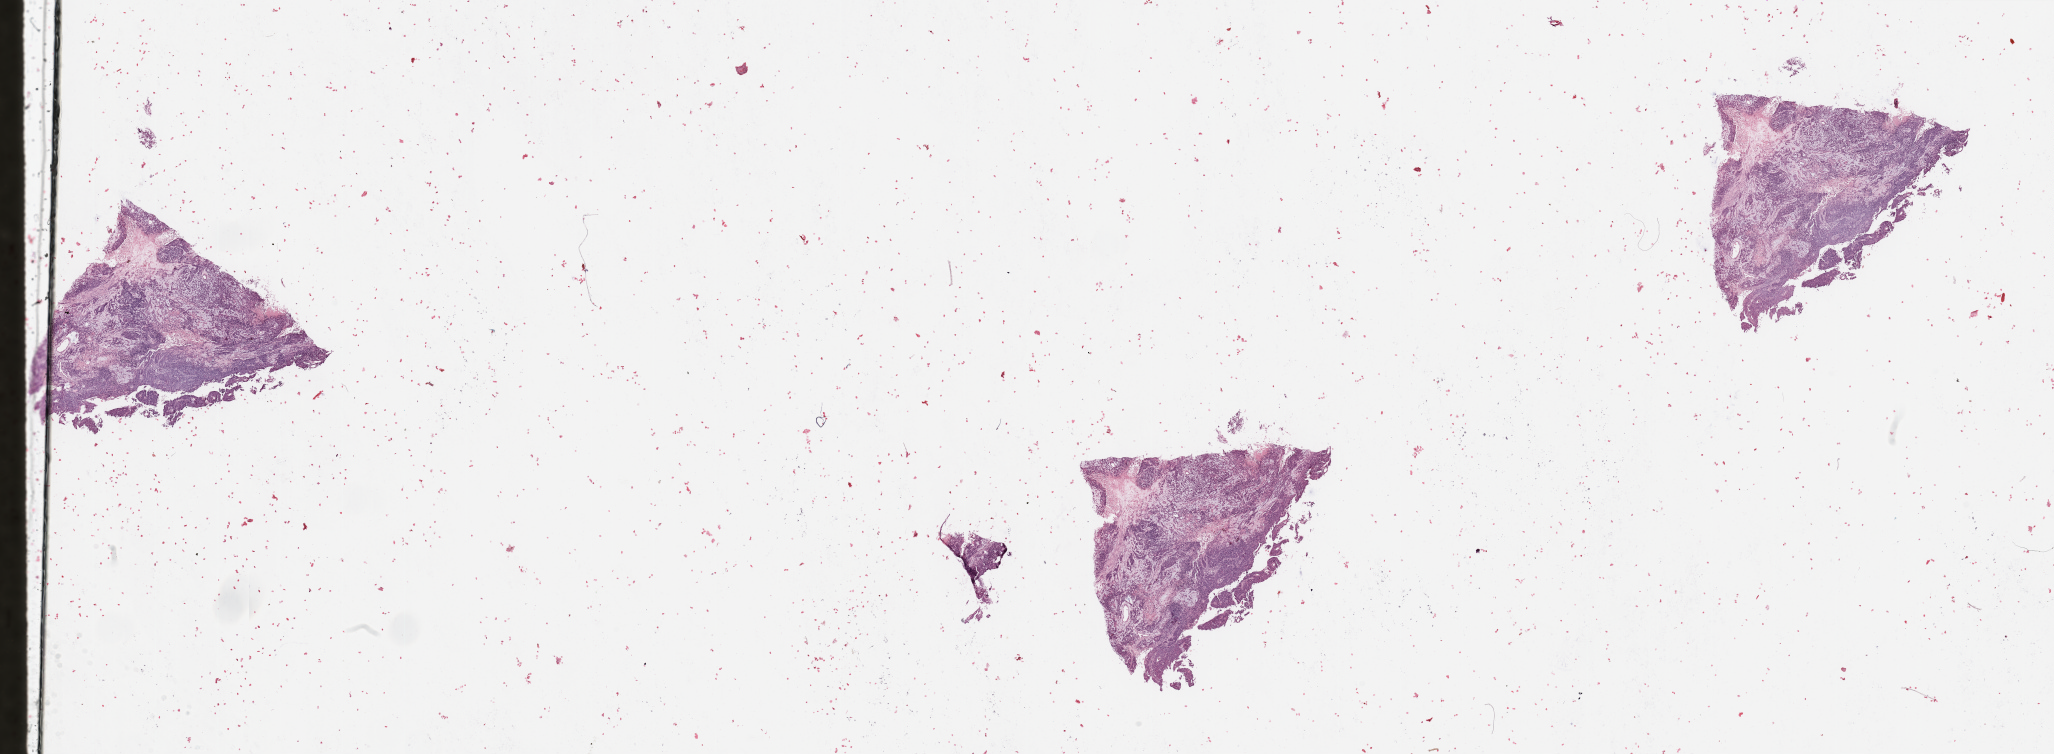
Hematoxylin and eosin (H&E) stained whole-slide image, whole scanned area (about 32.5 x 11.9 mm) shown as a low-resolution overview; tumour tissue sample, sampled site: uterus. Patient: female, age 59 years. Histologic grade: G3 (poorly differentiated). Slide review estimates, as recorded: tumour nuclei 80%, necrosis 5%.
• diagnosis: Endometrioid adenocarcinoma, NOS
• primary tumour site (as recorded): anterior endometrium
• AJCC pathologic stage: I